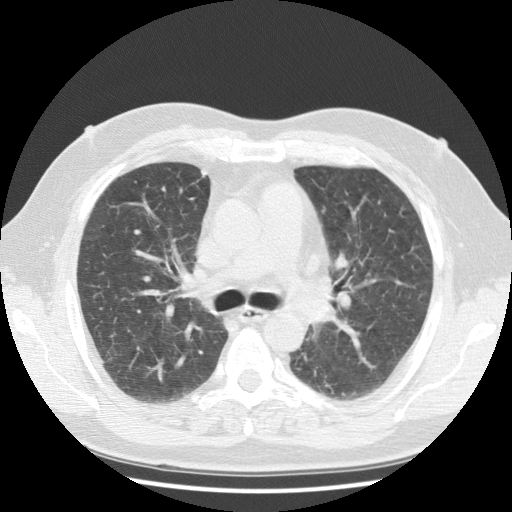
Low-dose screening chest CT, one axial slice; slice 70 of 108 in the series (ordered by position); 120 kVp; lung window (W 1500 / L -600 HU); 2.5 mm slice thickness; 512 × 512 image matrix, field of view 350 × 350 mm.
Outlined on this slice (manually delineated by an expert):
- lesion 1 (tumor, hilum of left lung): bounding box [x1, y1, x2, y2] px = [313, 300, 339, 321]